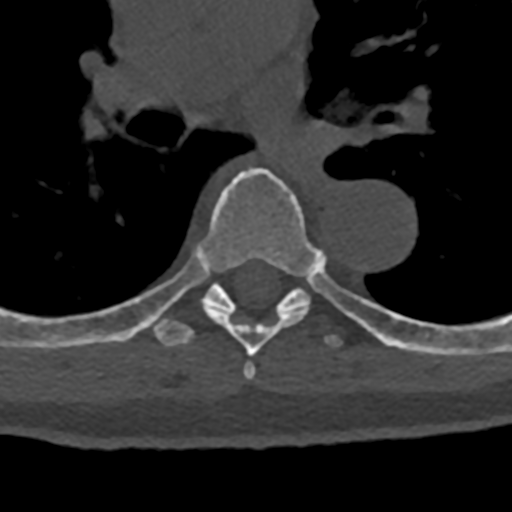
CT including the spine, one axial slice; slice 795 of 797 in the series (ordered by position); 120 kVp; bone window (W 1800 / L 400 HU); 512 × 512 image matrix, field of view 160 × 160 mm. Male patient, age 74 years. Case-level facts recorded for this patient, not image findings: primary cancer: renal; vertebrae with lytic lesions (as recorded): T10, L1, L2, L3, L4, L5.
Outlined on this slice (semi-automatic segmentation, software-assisted and operator-edited):
- T6 vertebra: bounding box <143,167,318,380> (left, top, right, bottom; pixels)
- T7 vertebra: <70,249,432,354>